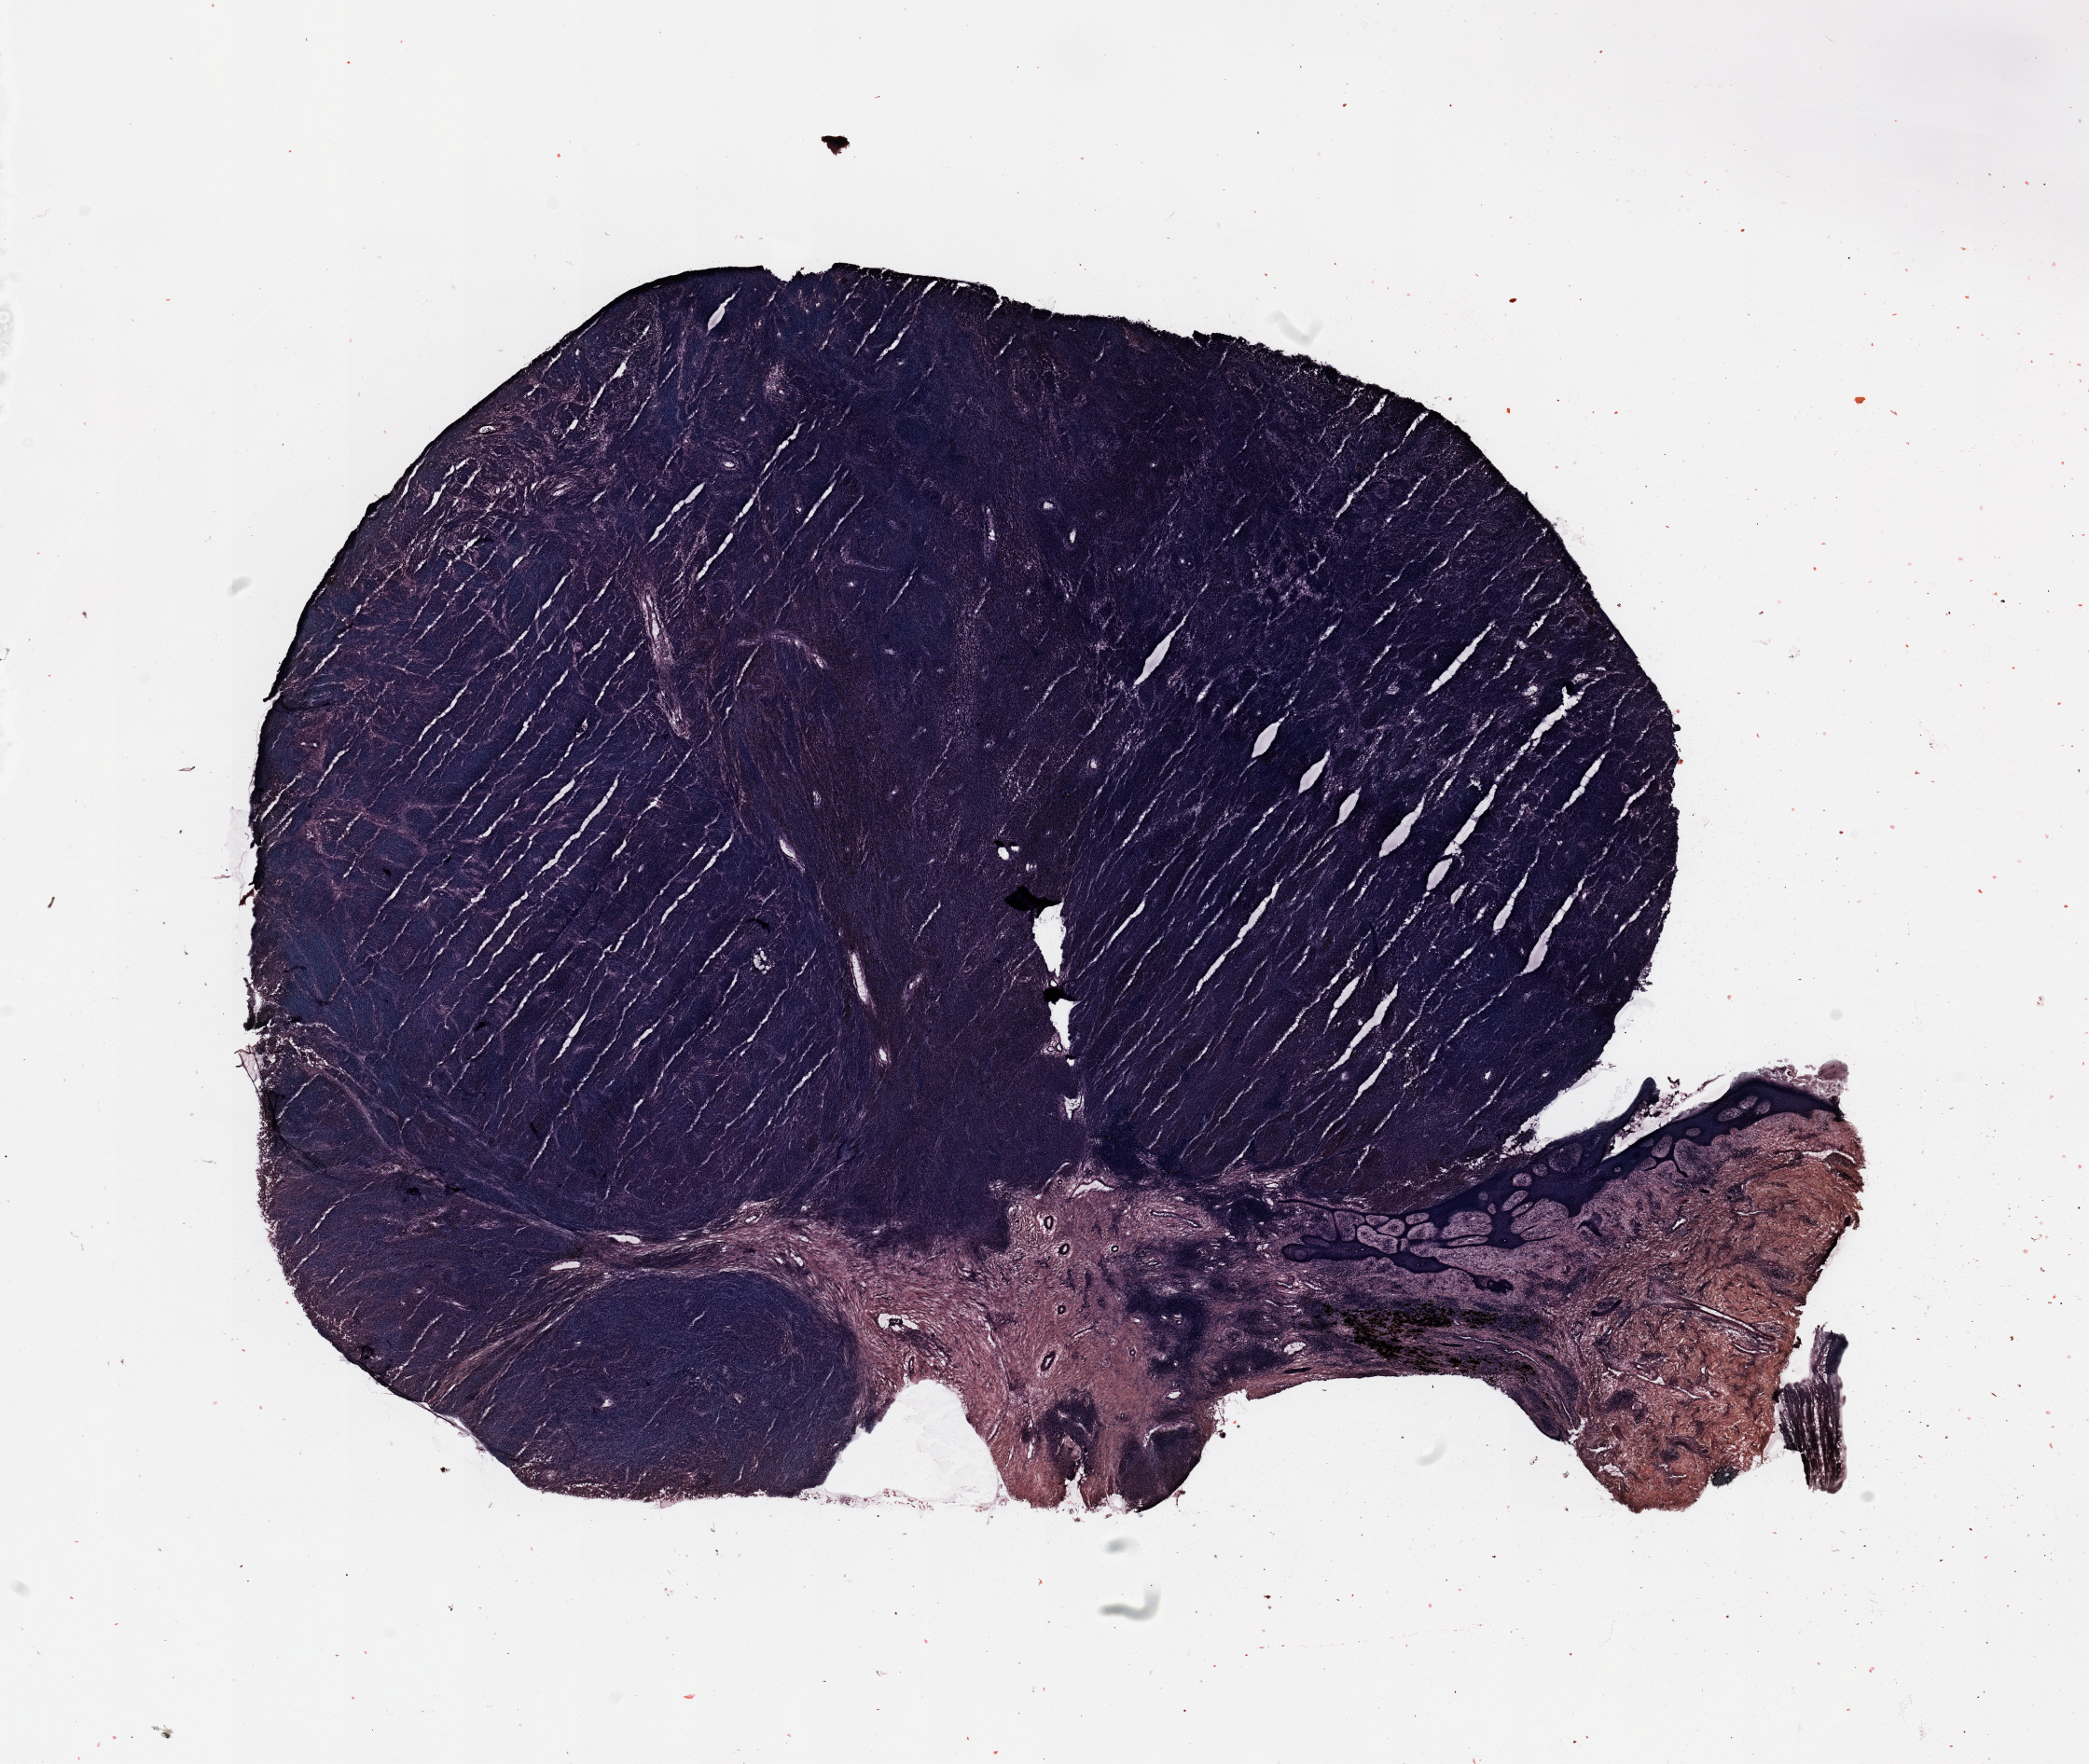
Hematoxylin and eosin (H&E) stained whole-slide image — low-resolution overview of the scanned area, about 17.7 x 15.0 mm, melanoma tumour tissue; sampled site not recorded. 67-year-old female patient.
• primary tumour site (as recorded): extremities
• patient diagnosis (cohort enrolment): cutaneous melanoma (skin)